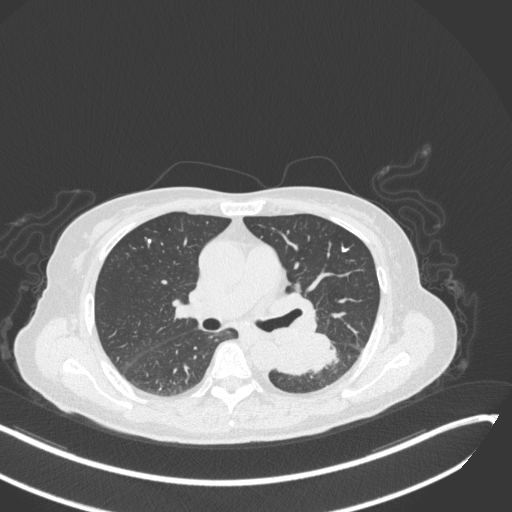
Chest CT, one axial slice. Position 163 of 342 along the scan axis. Lung window (W 1500 / L -600 HU). 1 mm slice thickness. 512 × 512 image matrix, field of view 400 × 400 mm. Patient: female, 64 years. Case-level facts recorded for this patient, not image findings: clinical TNM (as recorded): T3 N1 M1.
Annotated regions visible in this slice (bounding box drawn by a radiologist):
- lung tumour (recorded histology: small cell carcinoma): bounding box [x1, y1, x2, y2] px = [275, 331, 342, 376]